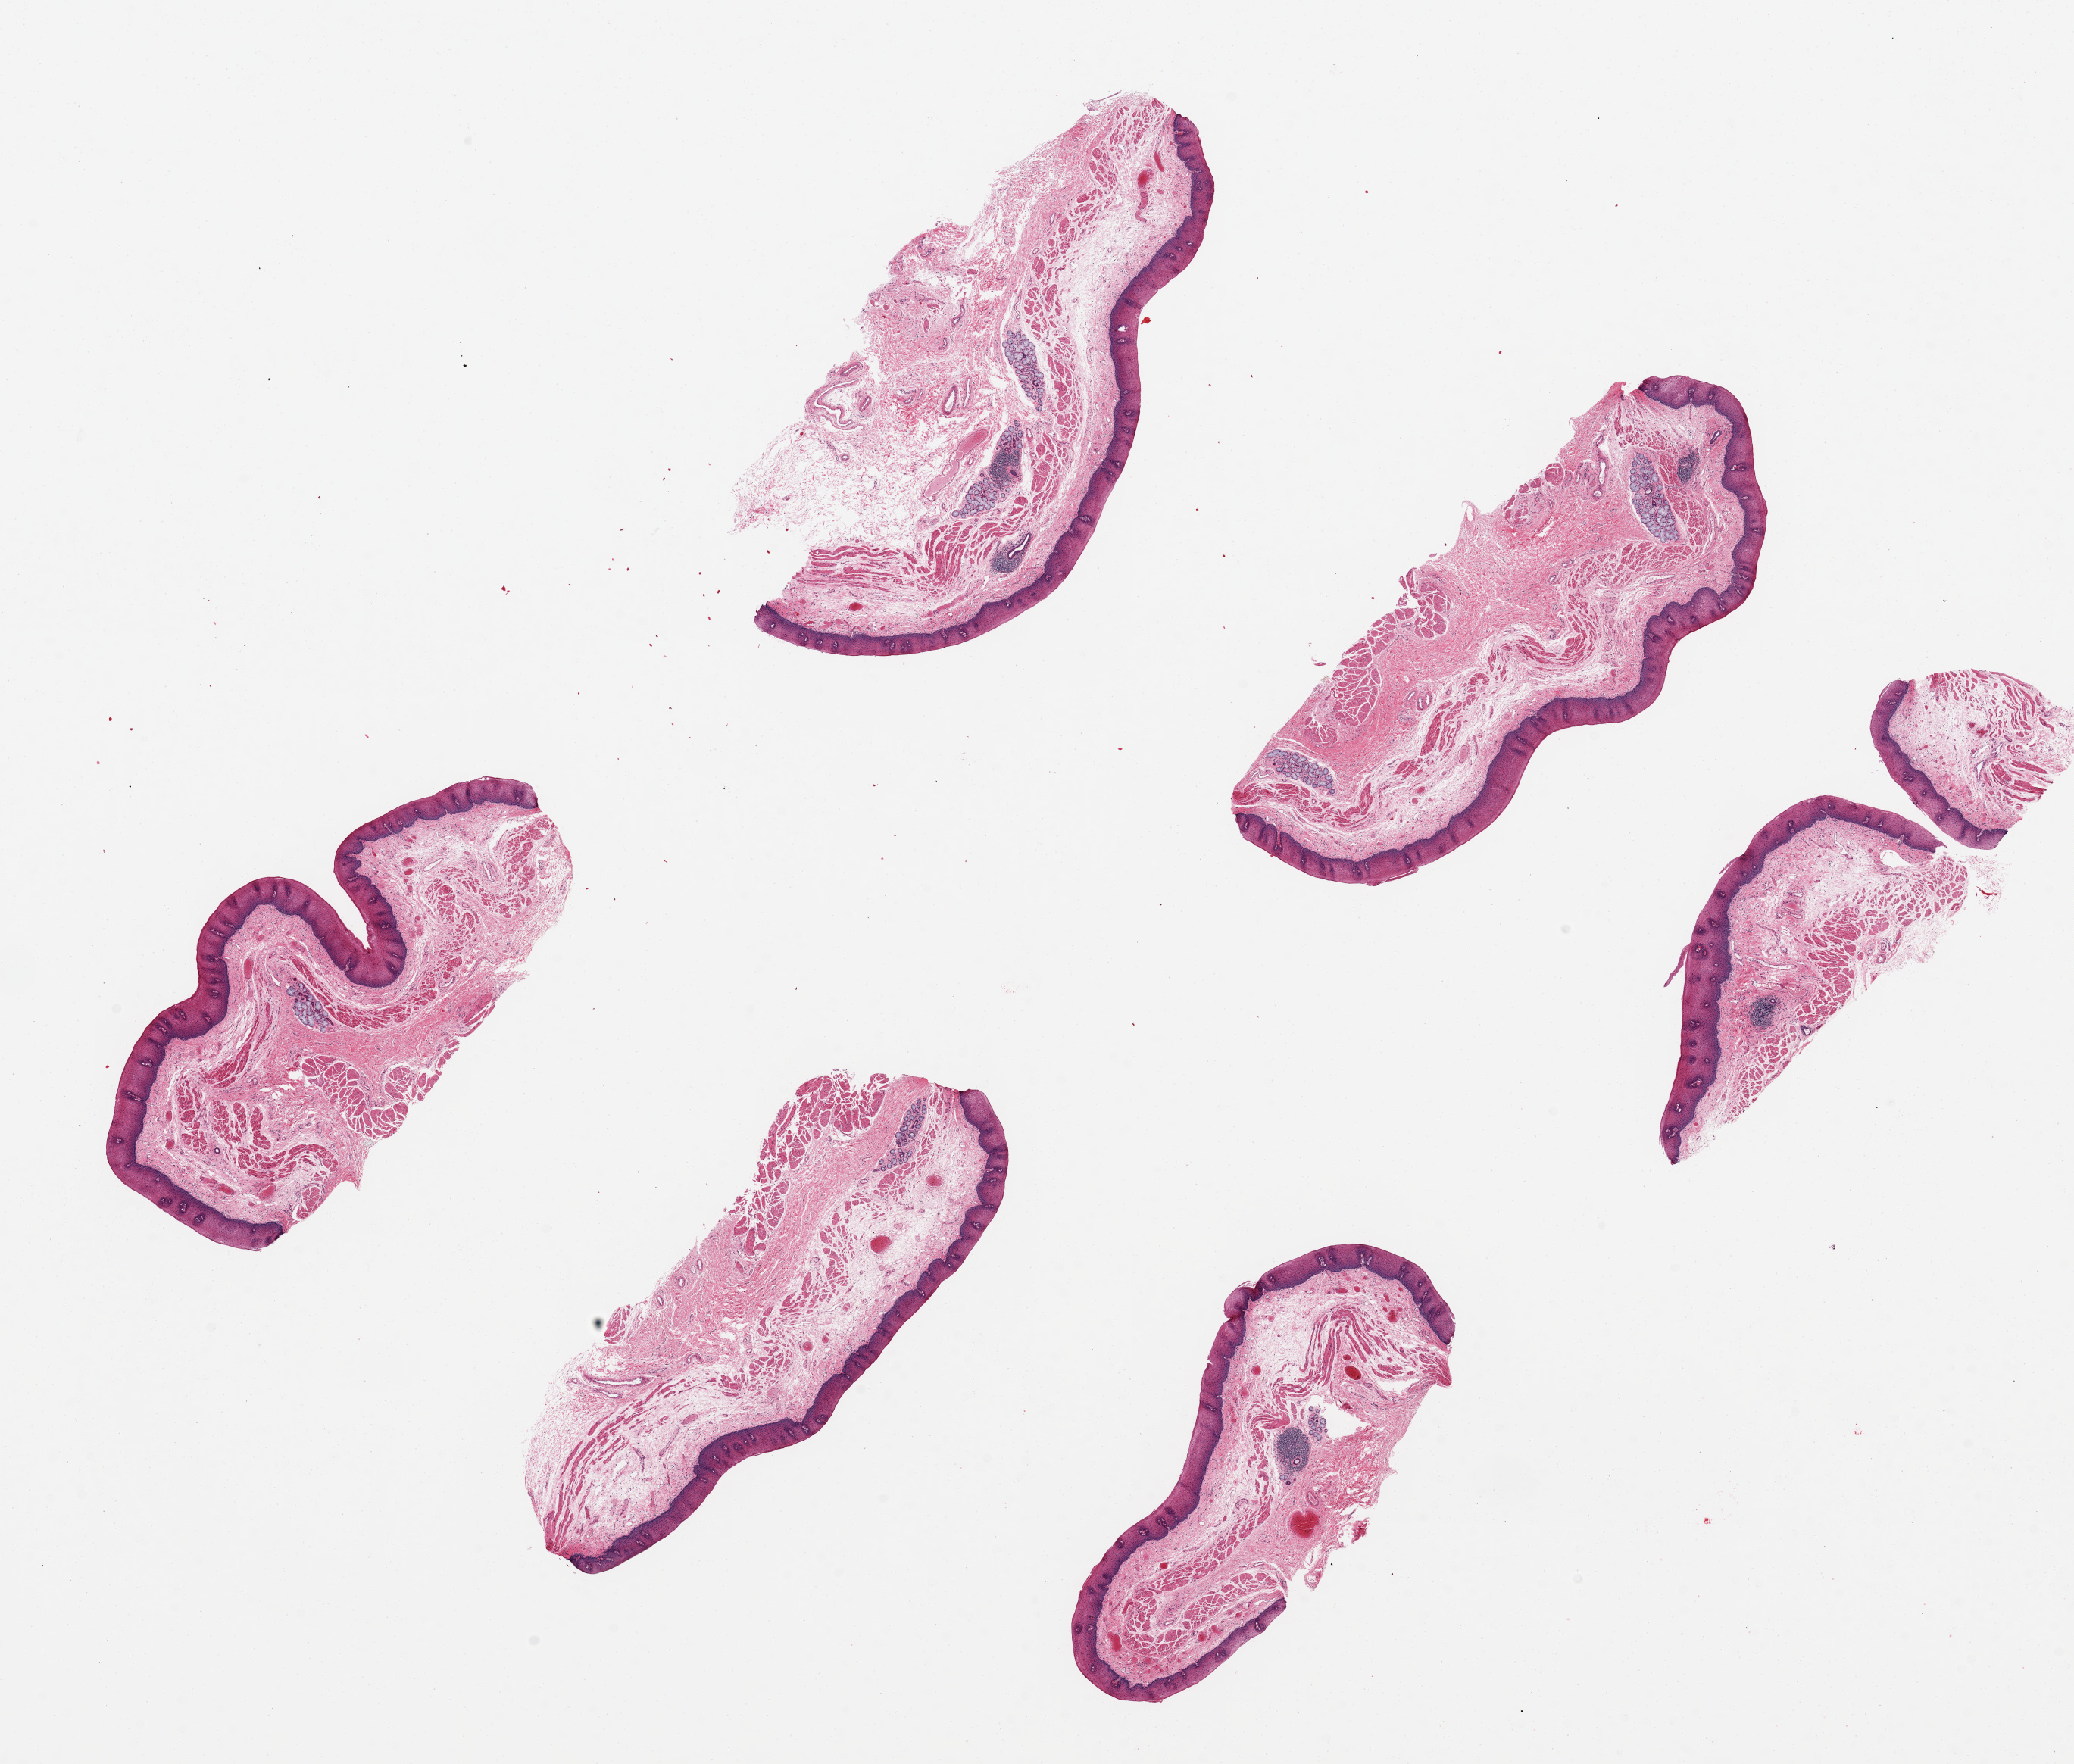
Whole-slide image, haematoxylin and eosin stain, brightfield, low-resolution overview of the scanned area, about 21.7 x 18.4 mm (from a 20x scan). PAXgene-fixed, paraffin-embedded tissue. Target tissue: esophageal mucous membrane. Tissue donor sample. Donor sex: male.
Reviewer comment on this tissue sample: 6 pieces up to 6.7x2.5 mm; well preserved, well cut.